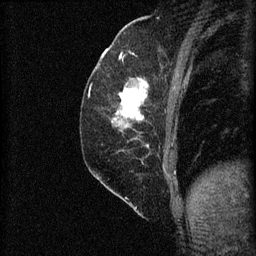
Breast MRI (dynamic contrast-enhanced), one sagittal slice. Position 25 of 60 along the scan axis. 3 images stored at this slice position (order not interpretable as contrast timing). 1.5 T. TE 4.2 ms, TR 8.2 ms. 2 mm slice thickness. 256 × 256 image matrix, field of view 180 × 180 mm. Female patient, age 59 years.
Annotated regions visible in this slice (semi-automatically segmented with operator editing):
- analysis volume of interest (the breast-tissue region the enhancement analysis was run in; not a lesion): bounding box <92,74,150,131> (left, top, right, bottom; pixels)
- tumour enhancement mask (voxels above the 70 % enhancement threshold inside the analysis volume of interest): <121,78,148,121>